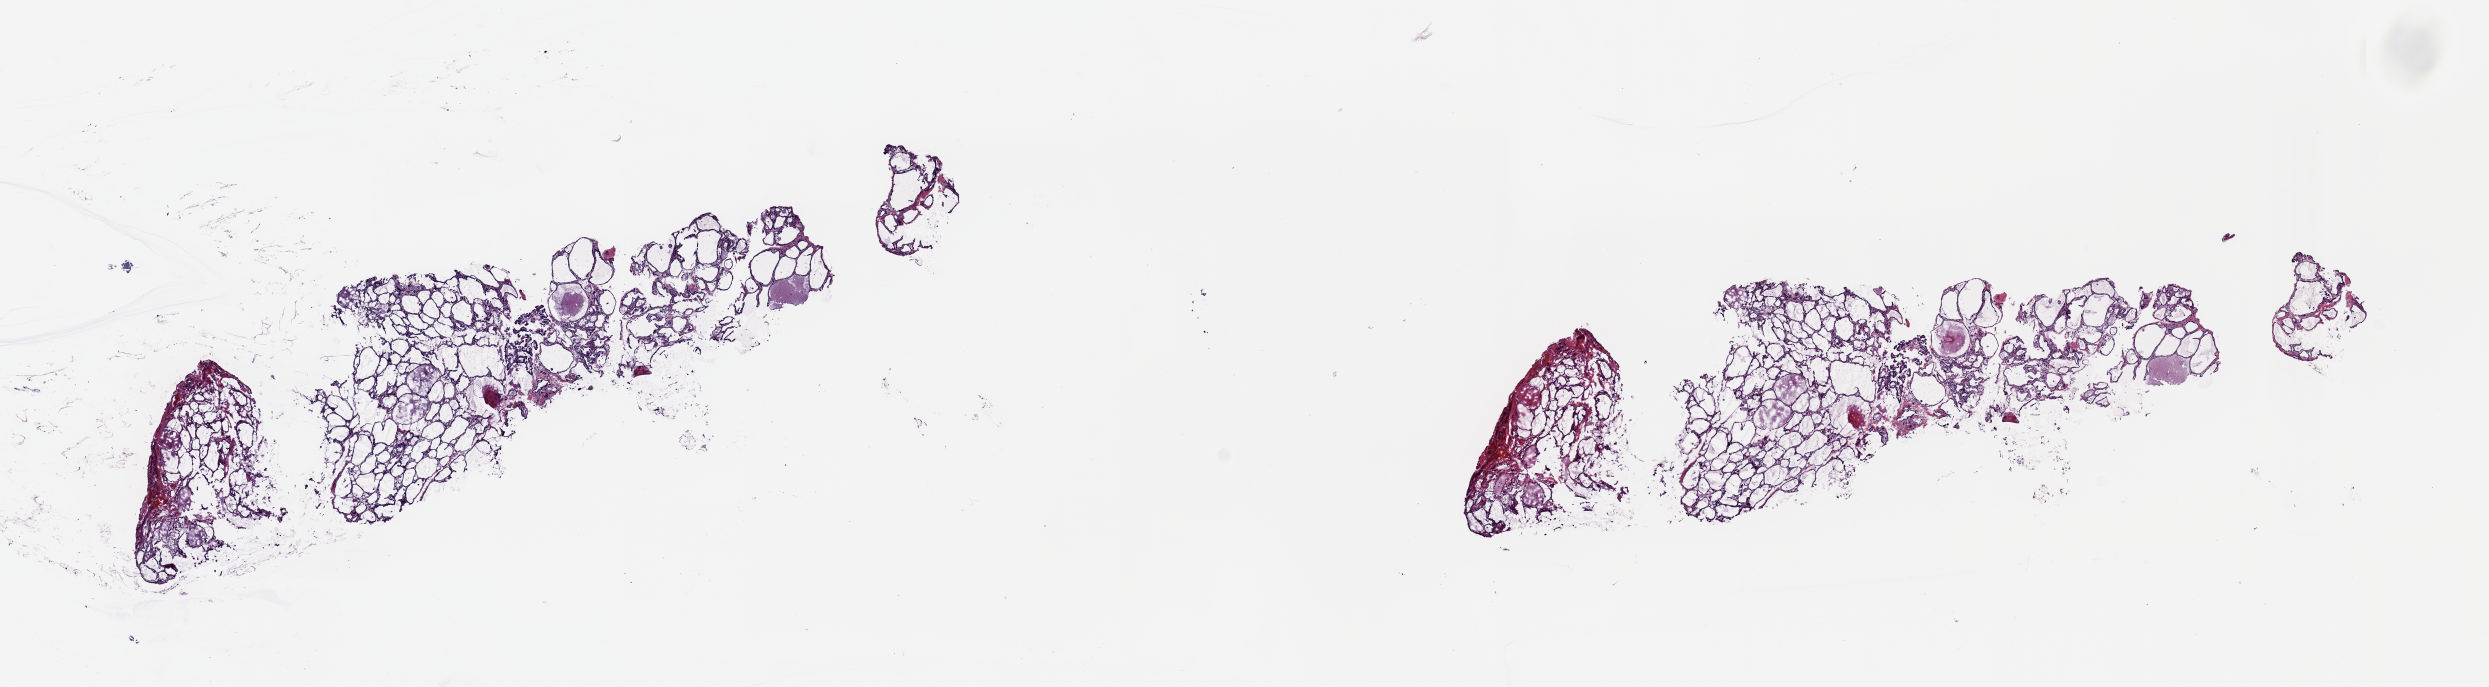
H&E-stained whole-slide image, whole scanned area (about 19.6 x 5.4 mm, slide scanned at 20x) shown as a low-resolution overview, frozen section from the top of the tissue portion, sample: solid tissue normal (non-tumour tissue), thyroid. Male, age 27 years at initial diagnosis. Composition of this section per pathologist review: tumour cells 0%, tumour nuclei 0%, normal cells 99%, stromal cells 1%, necrosis 0%. Infiltration values recorded for this section: lymphocyte infiltration 0%, monocyte infiltration 0%, neutrophil infiltration 0%.
This section: solid tissue normal sample (biorepository sample class). Patient diagnosis: Papillary adenocarcinoma, NOS (thyroid gland).